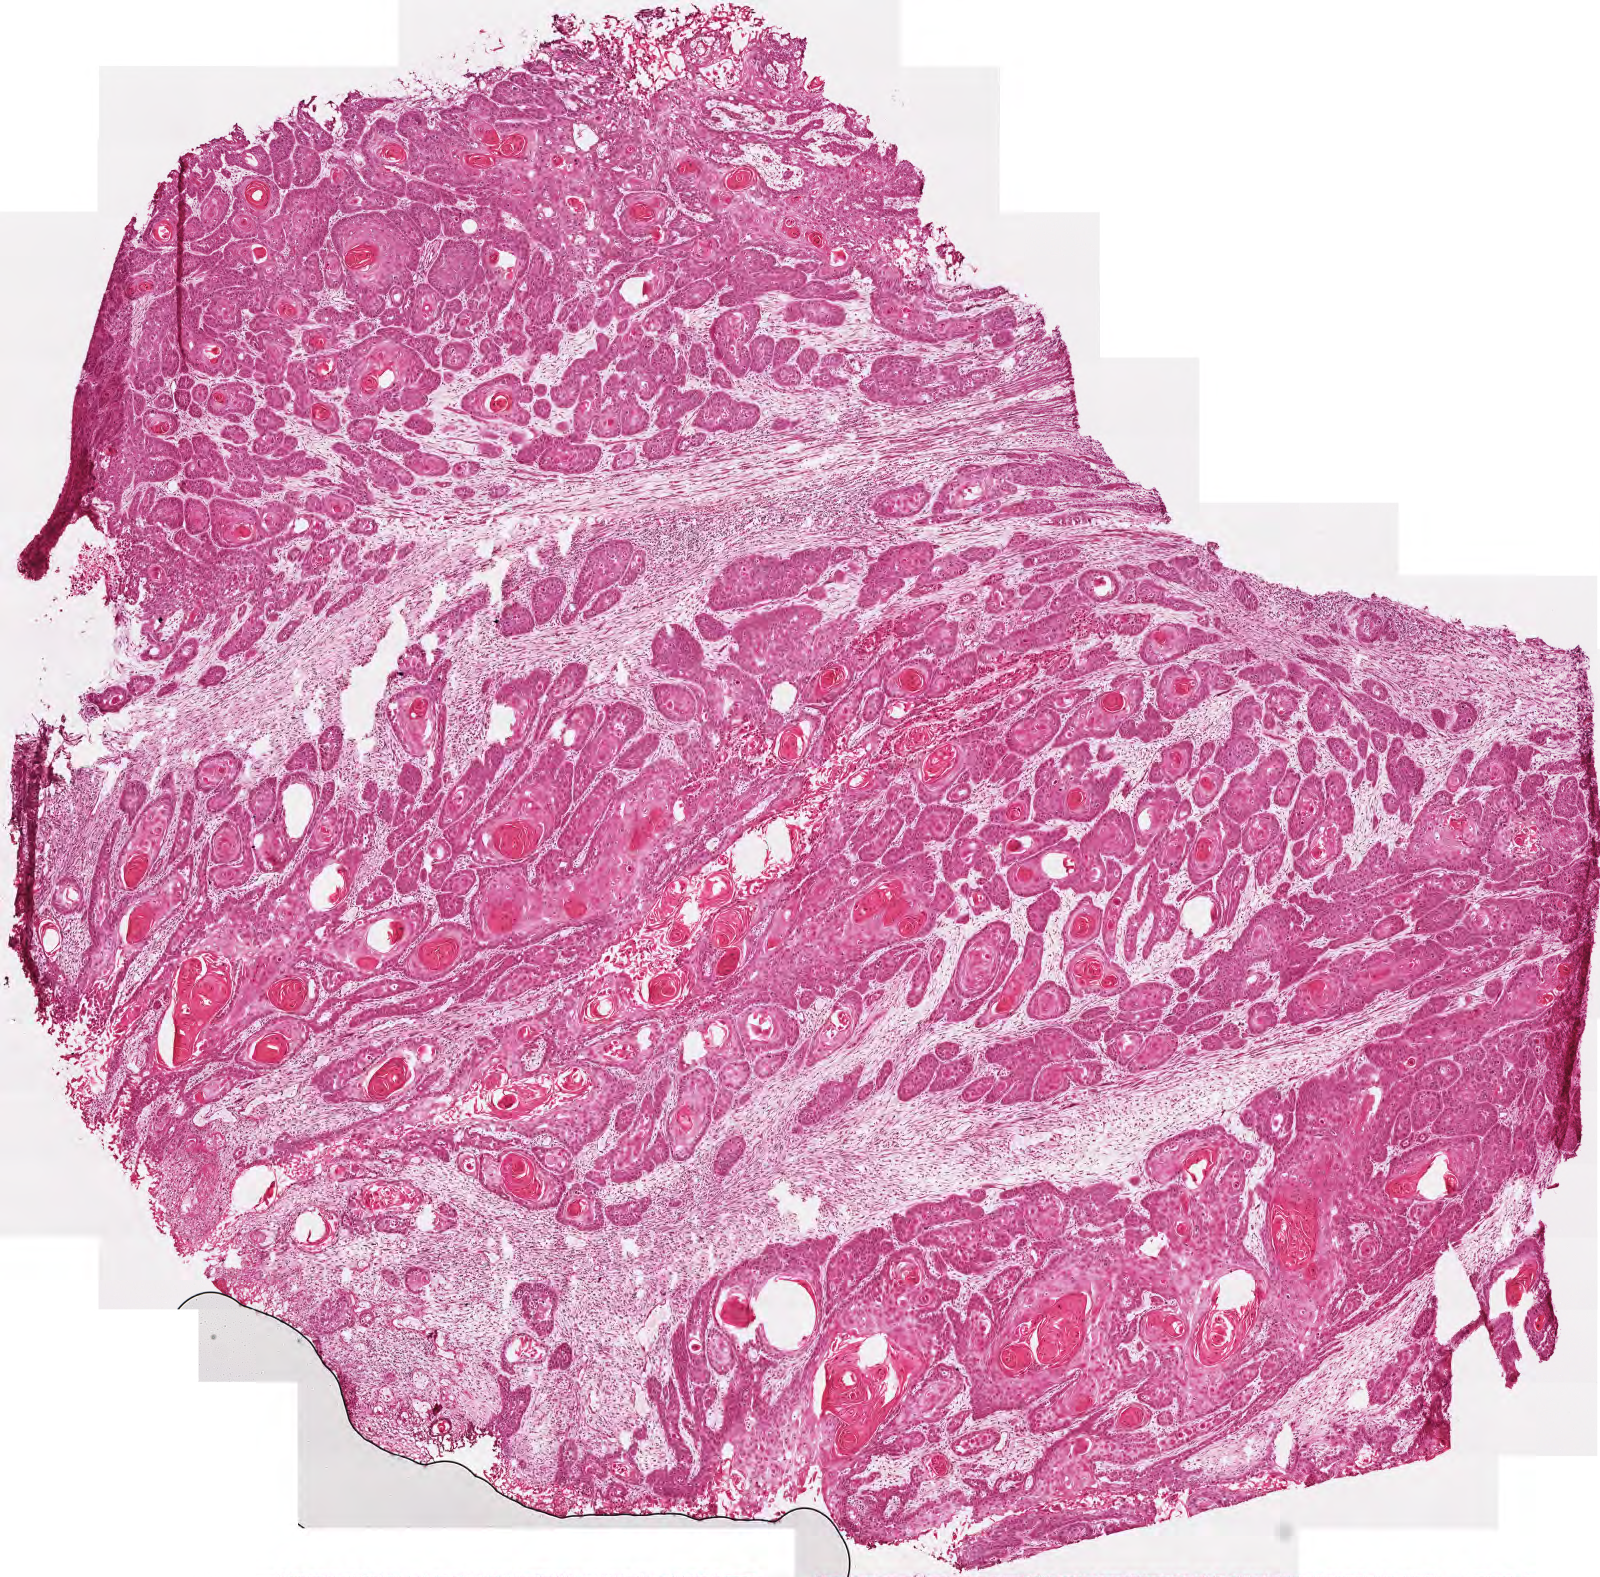
Whole-slide histology image, Hematoxylin and eosin (H&E) stained, a low-resolution overview of the entire scanned area, about 3.2 x 3.2 mm; frozen section from the top of the tissue portion; head and neck, primary tumour sample. Male, age 60 years at initial diagnosis. Histologic grade: G2 (moderately differentiated). Slide review estimates, as recorded: tumour cells 85%, tumour nuclei 75%, normal cells 0%, stromal cells 15%, necrosis 0%.
Lymph nodes positive (case pathology): 0 of 45 examined. AJCC pathologic stage: IVA (6th edition). Diagnosis: Squamous cell carcinoma, NOS (overlapping lesion of lip, oral cavity and pharynx).